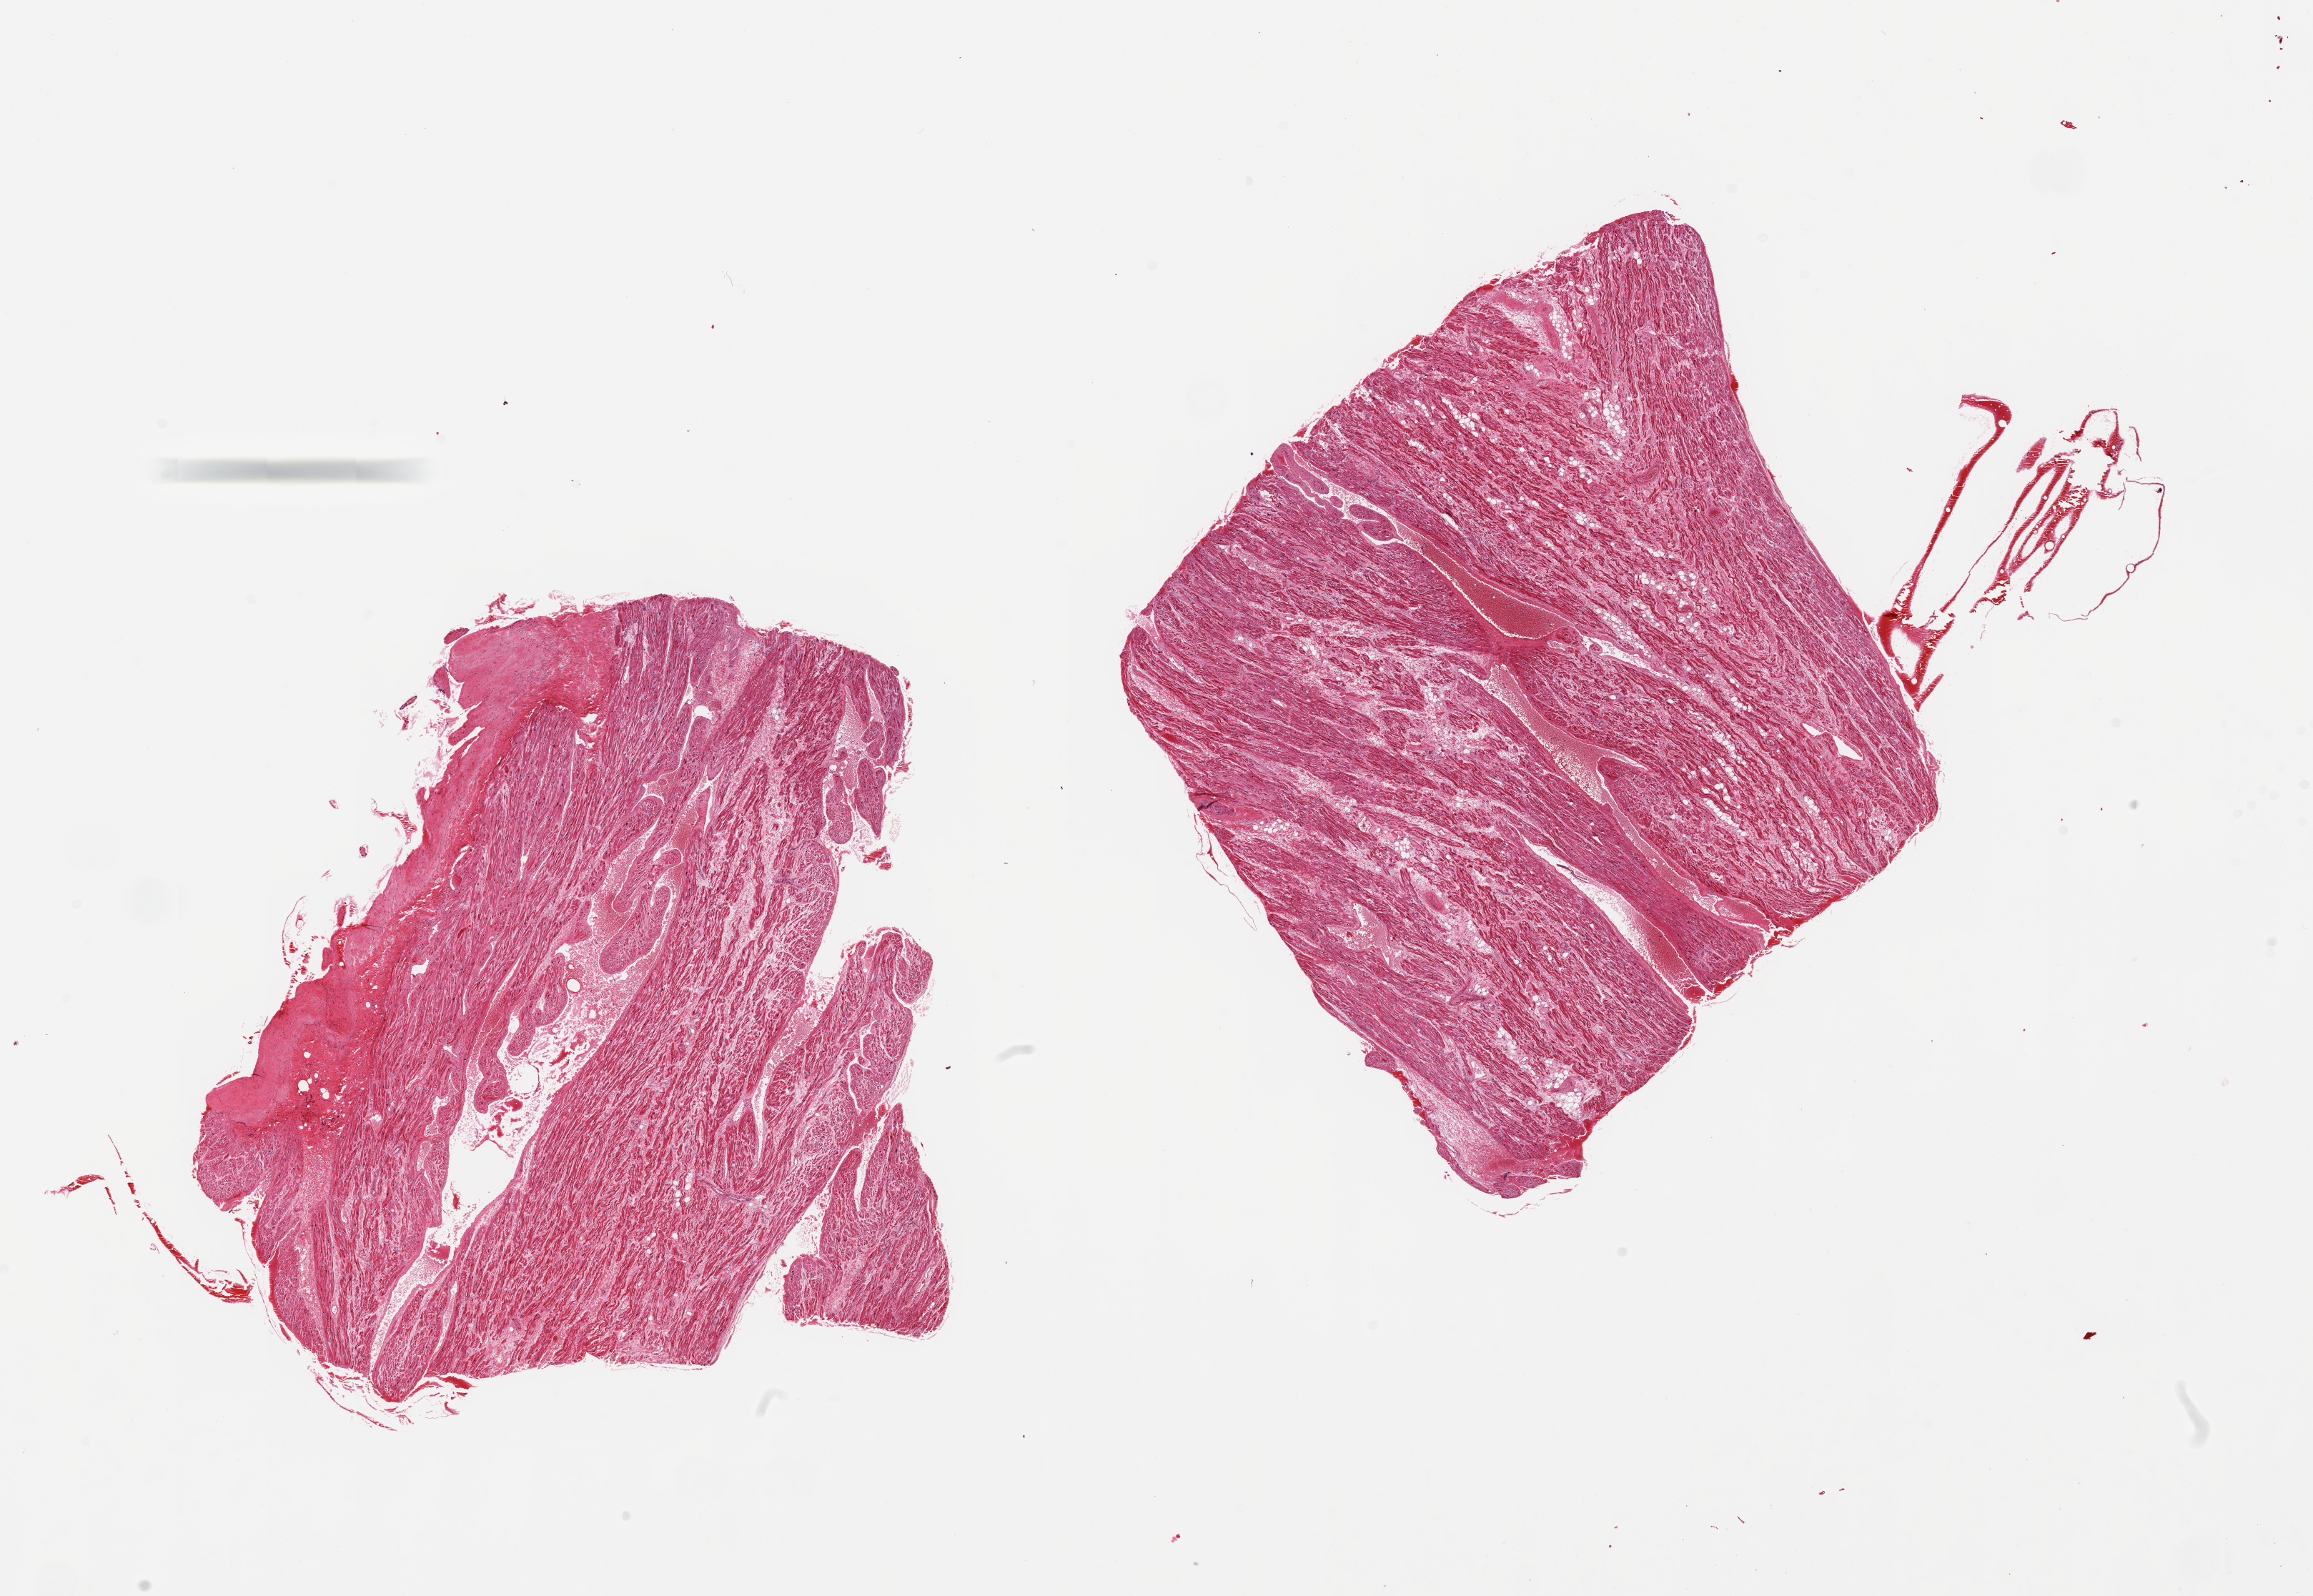
Digitized hematoxylin and eosin (H&E)-stained section, brightfield — shown as a low-resolution overview of the whole scanned area (about 25.6 x 17.7 mm, acquisition: 20x scan). PAXgene-fixed, paraffin-embedded tissue. Section of auricular appendage (target tissue). Tissue donor sample. Male donor.
- reviewer comment on this tissue sample: 2 pieces, ~20% of internal fat, interstitial fibrosis and myocyte hypertrophy